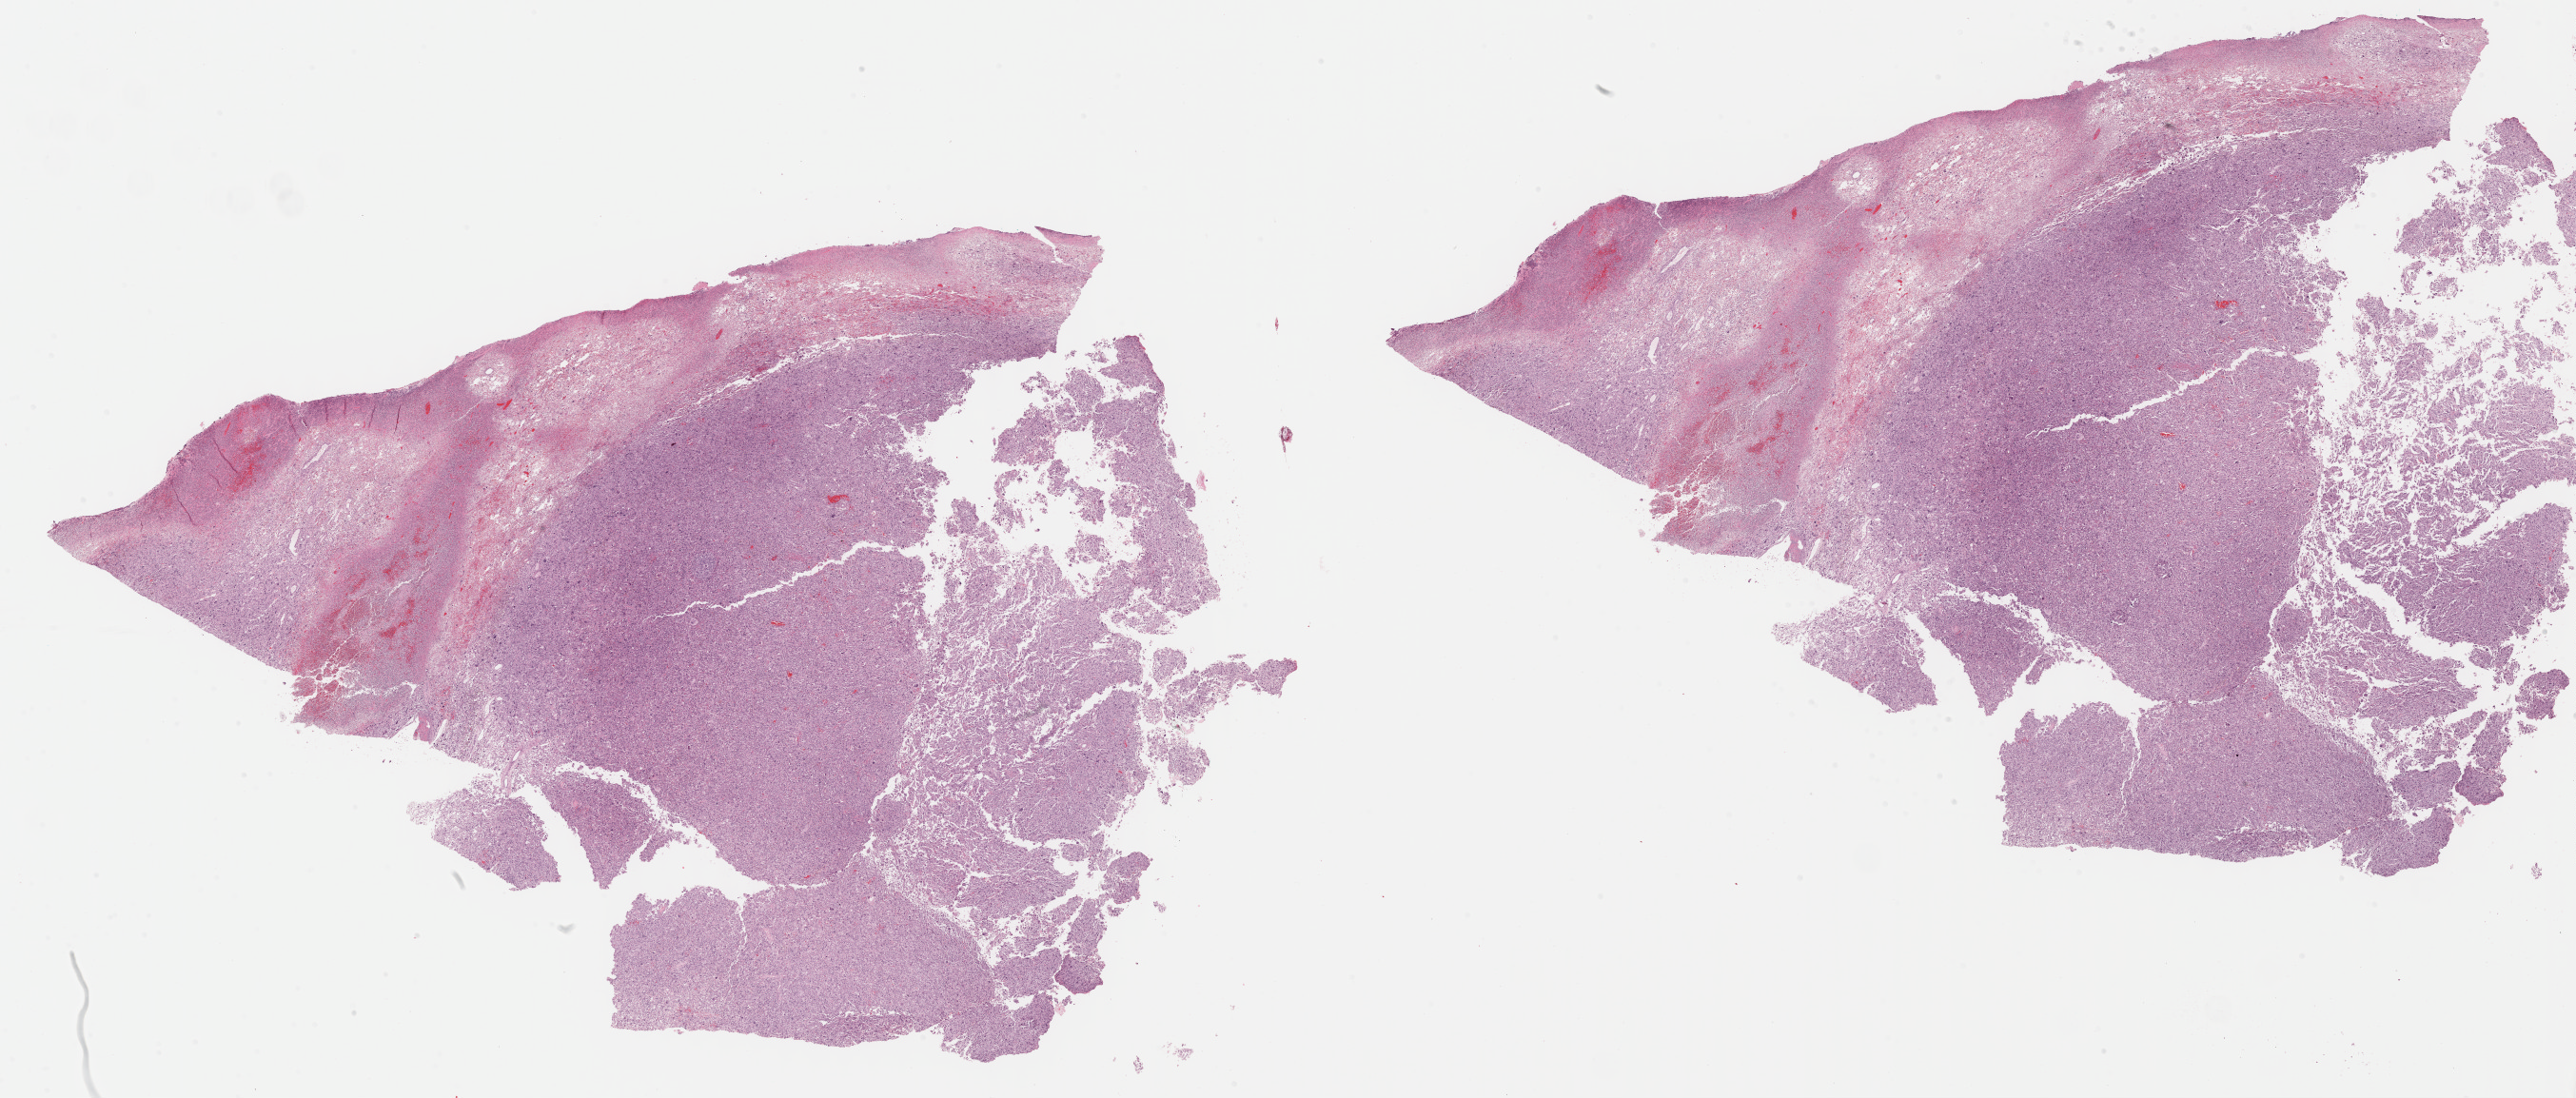
Digitized H&E-stained tissue section (whole slide) — whole scanned area (about 43.8 x 18.7 mm, slide scanned at 40x) shown as a low-resolution overview, formalin-fixed paraffin-embedded (FFPE) diagnostic section, connective, subcutaneous and other soft tissues, primary tumour sample. Female, age 65 years at initial diagnosis.
- diagnosis: Malignant fibrous histiocytoma (connective, subcutaneous and other soft tissues of lower limb and hip)